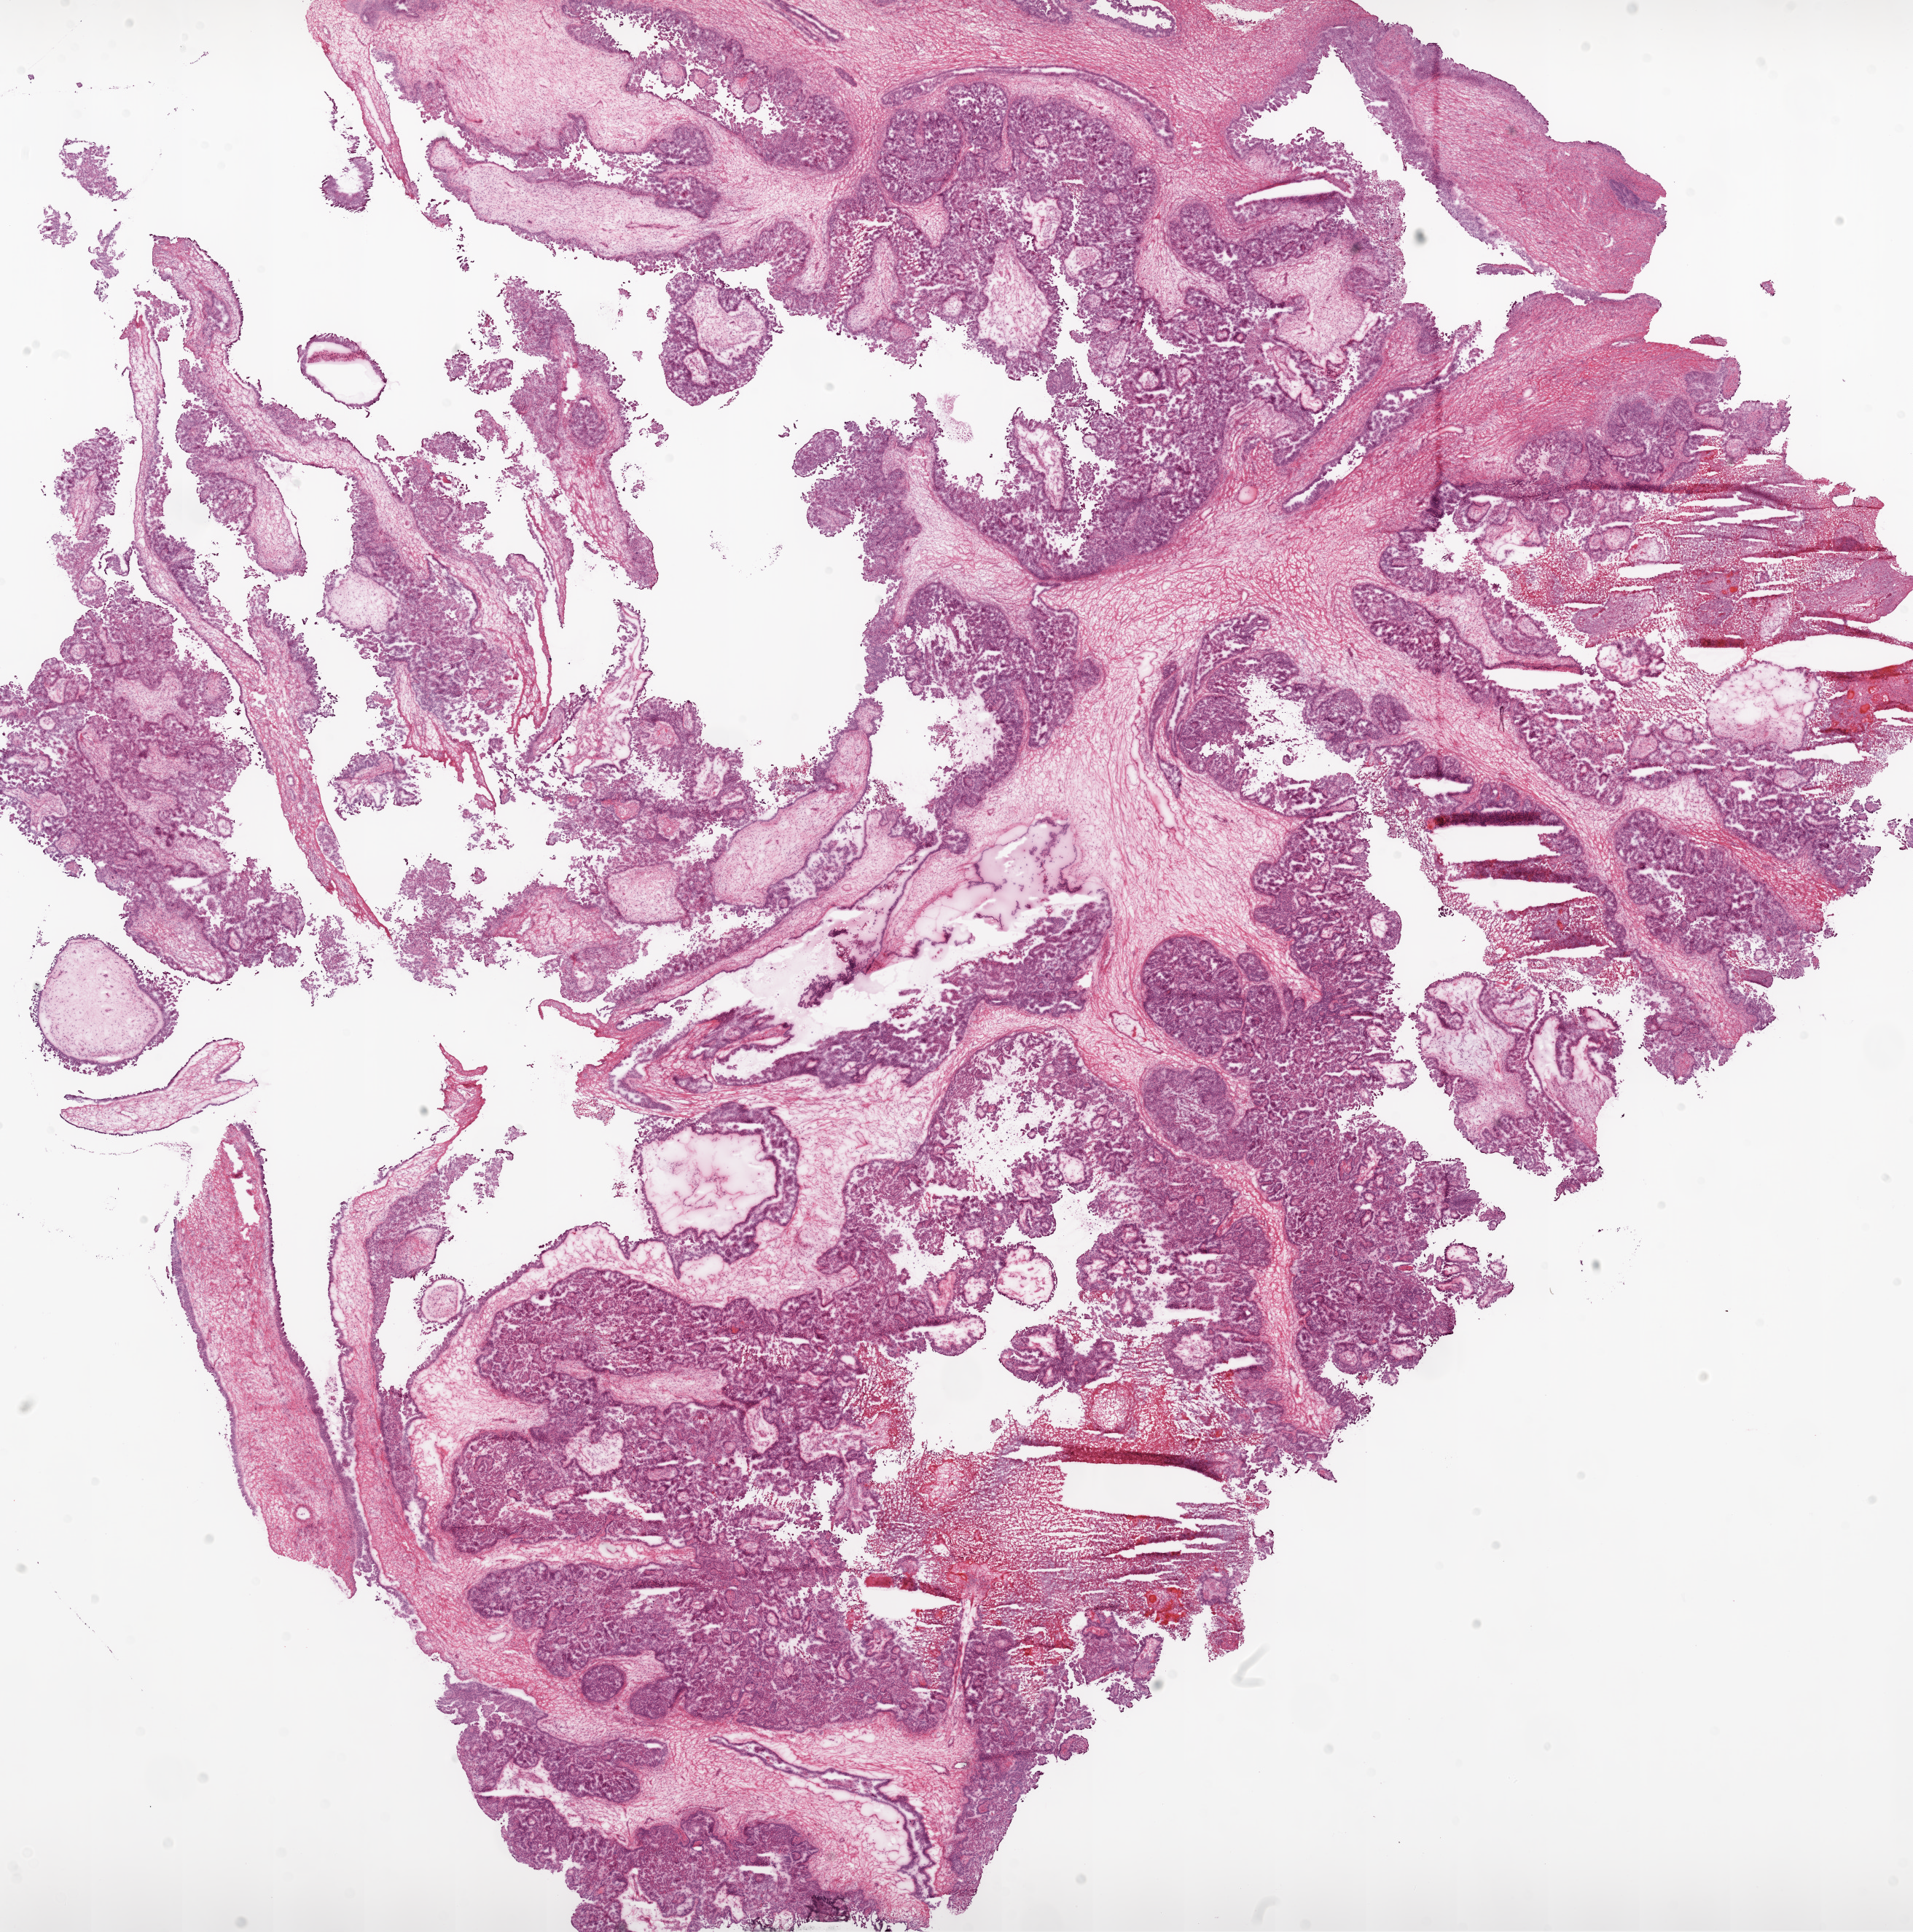
Digitized Hematoxylin and eosin (H&E) stained tissue section (whole slide) — shown as a low-resolution overview of the whole scanned area (about 21.1 x 21.3 mm); frozen section from the top of the tissue portion; primary tumour sample from the ovary. Female, age 73 years at initial diagnosis. Histologic grade: G3 (poorly differentiated). Composition of this section per pathologist review: tumour cells 80%, tumour nuclei 90%, normal cells 0%, stromal cells 10%, necrosis 10%.
FIGO stage: IIIC. Diagnosis: Serous cystadenocarcinoma, NOS. Laterality: bilateral.